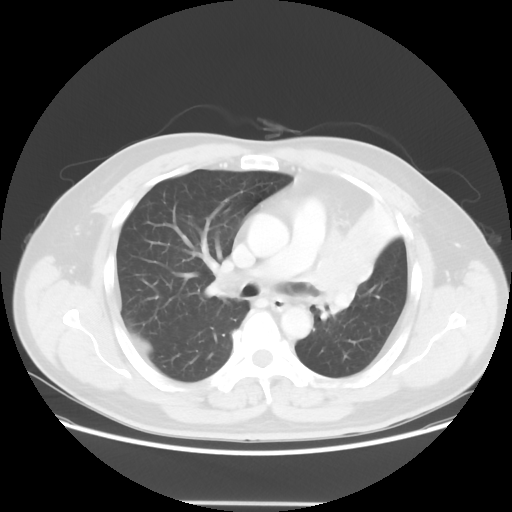
Chest CT, one axial slice. Slice 38 of 62 in the series (ordered by position). 120 kVp. Lung window (W 1500 / L -600 HU). 5 mm slice thickness. 512 × 512 image matrix. Male patient, age 49 years. From the clinical record (not read from this slice): clinical TNM (as recorded): T3 N3 M1c.
Structures marked on this image (bounding box drawn by a radiologist):
- lung tumour (recorded histology: squamous cell carcinoma): bounding box [x1, y1, x2, y2] px = [318, 230, 382, 315]